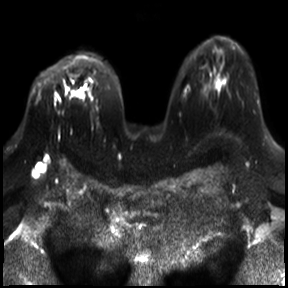
Breast MRI, one axial slice. Slice 21 of 30 in the series (ordered by position). Diffusion-weighted series; image 2 of 4 stored at this slice position (different b-values; order by instance number). 3 T. 4 mm slice thickness. 288 × 288 image matrix. Female patient.
Outlined on this slice (outlined manually by an expert reader):
- tumour on diffusion-weighted imaging: box from (x=65, y=88) to (x=81, y=98) px